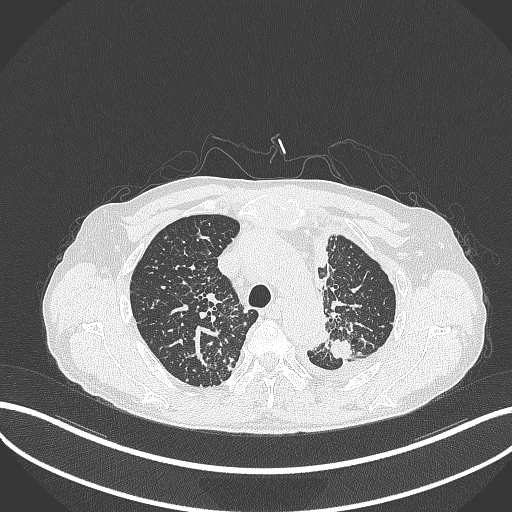
Chest CT, one axial slice. 120 kVp. Lung window (W 1500 / L -600 HU). 1 mm slice thickness. 512 × 512 image matrix, field of view 400 × 400 mm. Male patient, age 58 years. Case-level facts recorded for this patient, not image findings: clinical TNM (as recorded): T1c N3 M1.
Outlined on this slice (bounding box drawn by a radiologist):
- lung tumour (recorded histology: adenocarcinoma): bounding box <324,336,354,361> (left, top, right, bottom; pixels)